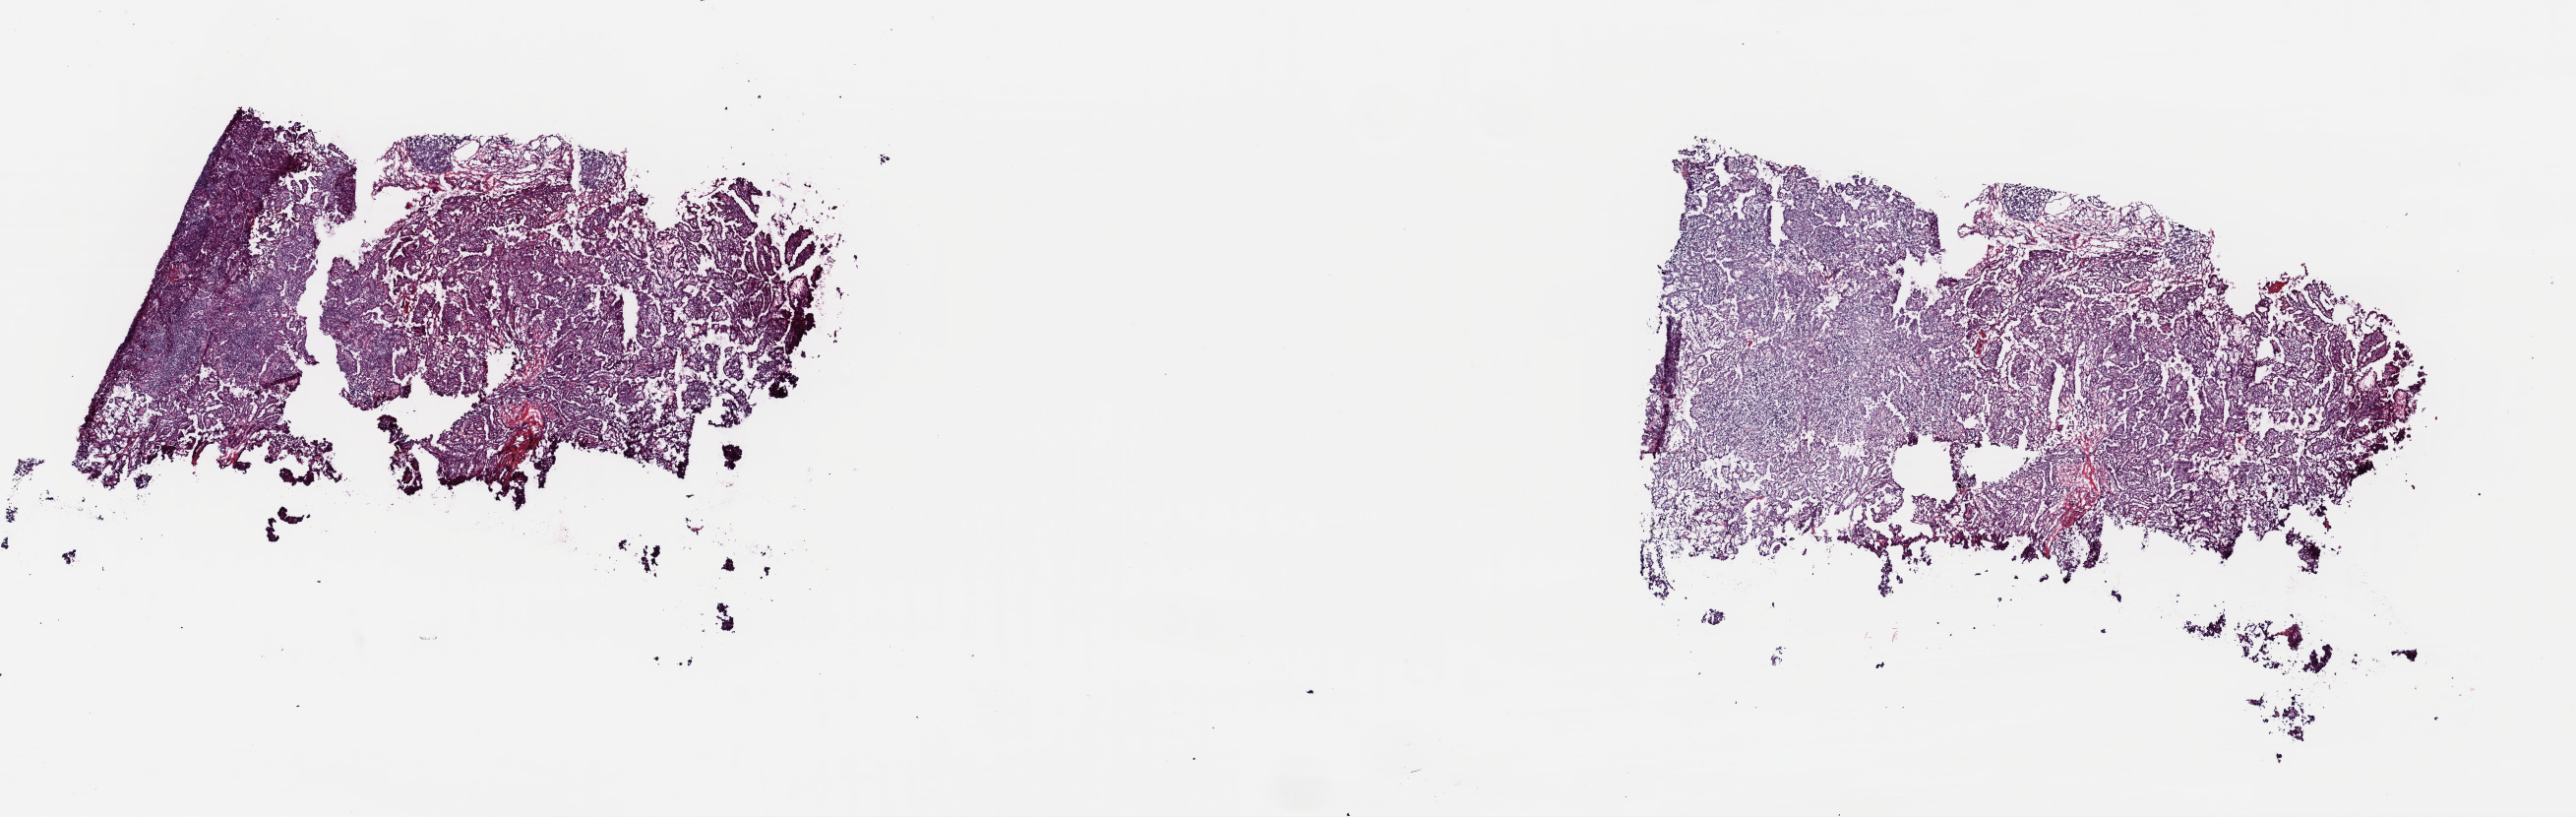
Digitized Hematoxylin and eosin (H&E) stained tissue section (whole slide) — shown as a low-resolution overview of the whole scanned area (about 20.7 x 6.6 mm, acquisition: 40x scan). Frozen section. Sample: primary tumour, thyroid. Female patient; age at initial diagnosis 33 years. Composition of this section per pathologist review: tumour cells 95%, tumour nuclei 95%, normal cells 0%, stromal cells 5%, necrosis 0%. Inflammatory infiltration, as recorded: lymphocyte infiltration 1%, monocyte infiltration 0%, neutrophil infiltration 0%.
- diagnosis: Papillary adenocarcinoma, NOS
- AJCC pathologic stage: I (6th edition)
- TNM: T2 NX MX